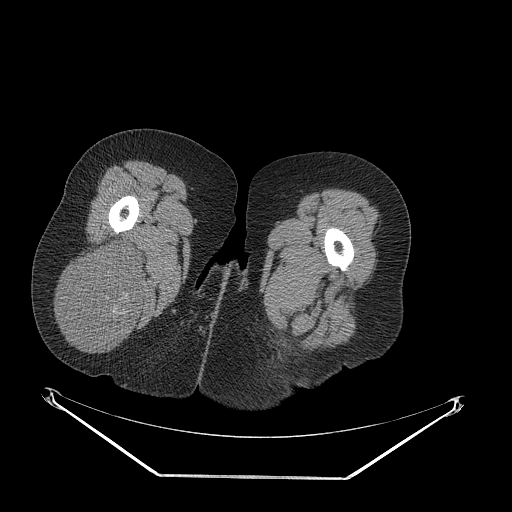
CT of an extremity soft-tissue mass (from a PET/CT study), one axial slice. Slice 42 of 257 in the series (ordered by position). Soft-tissue window (W 400 / L 40 HU). 3.75 mm slice thickness. 512 × 512 image matrix, field of view 500 × 500 mm. Female patient. From the clinical record (not read from this slice): histological type: synovial sarcoma; grade: intermediate; site of the primary tumour: right buttock.
Outlined on this slice (expert contour drawn on MRI and transferred to this co-registered scan by the dataset authors):
- gross tumour volume including surrounding oedema: bounding box (x1, y1, x2, y2) in pixels: (62, 246, 145, 346)
- gross tumour volume (mass): (62, 246, 145, 346)